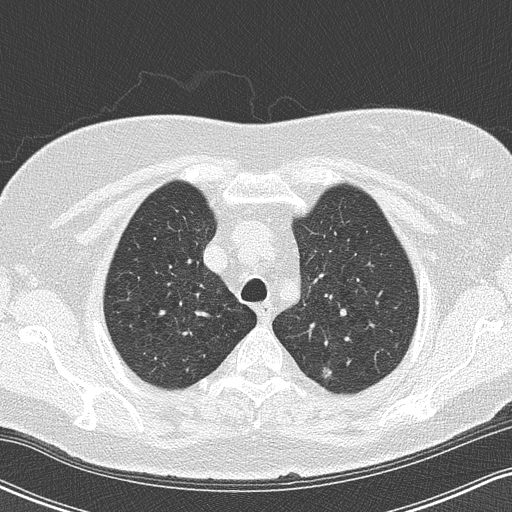
Low-dose screening chest CT, axial slice; third annual screen; lung window (W 1500 / L -600 HU); 2 mm slice thickness; slice 26 of 155 in the series. Female participant, aged 65 years at enrolment. Former smoker at enrolment.
Lesion marked by an expert reader, bounding box [x1, y1, x2, y2] px = [305, 356, 349, 393]. The exam's reader record, not a measurement of the box and not confirmed to be the same lesion: non-calcified nodule or mass ≥4 mm, left upper lobe, 8 × 6 mm, pre-existing on the prior screen: yes. Participant outcome: lung cancer diagnosed 103 days after this screen — adenocarcinoma, NOS, left upper lobe, moderately differentiated (G2), stage IA (AJCC 6th edition), 8 mm at pathology.